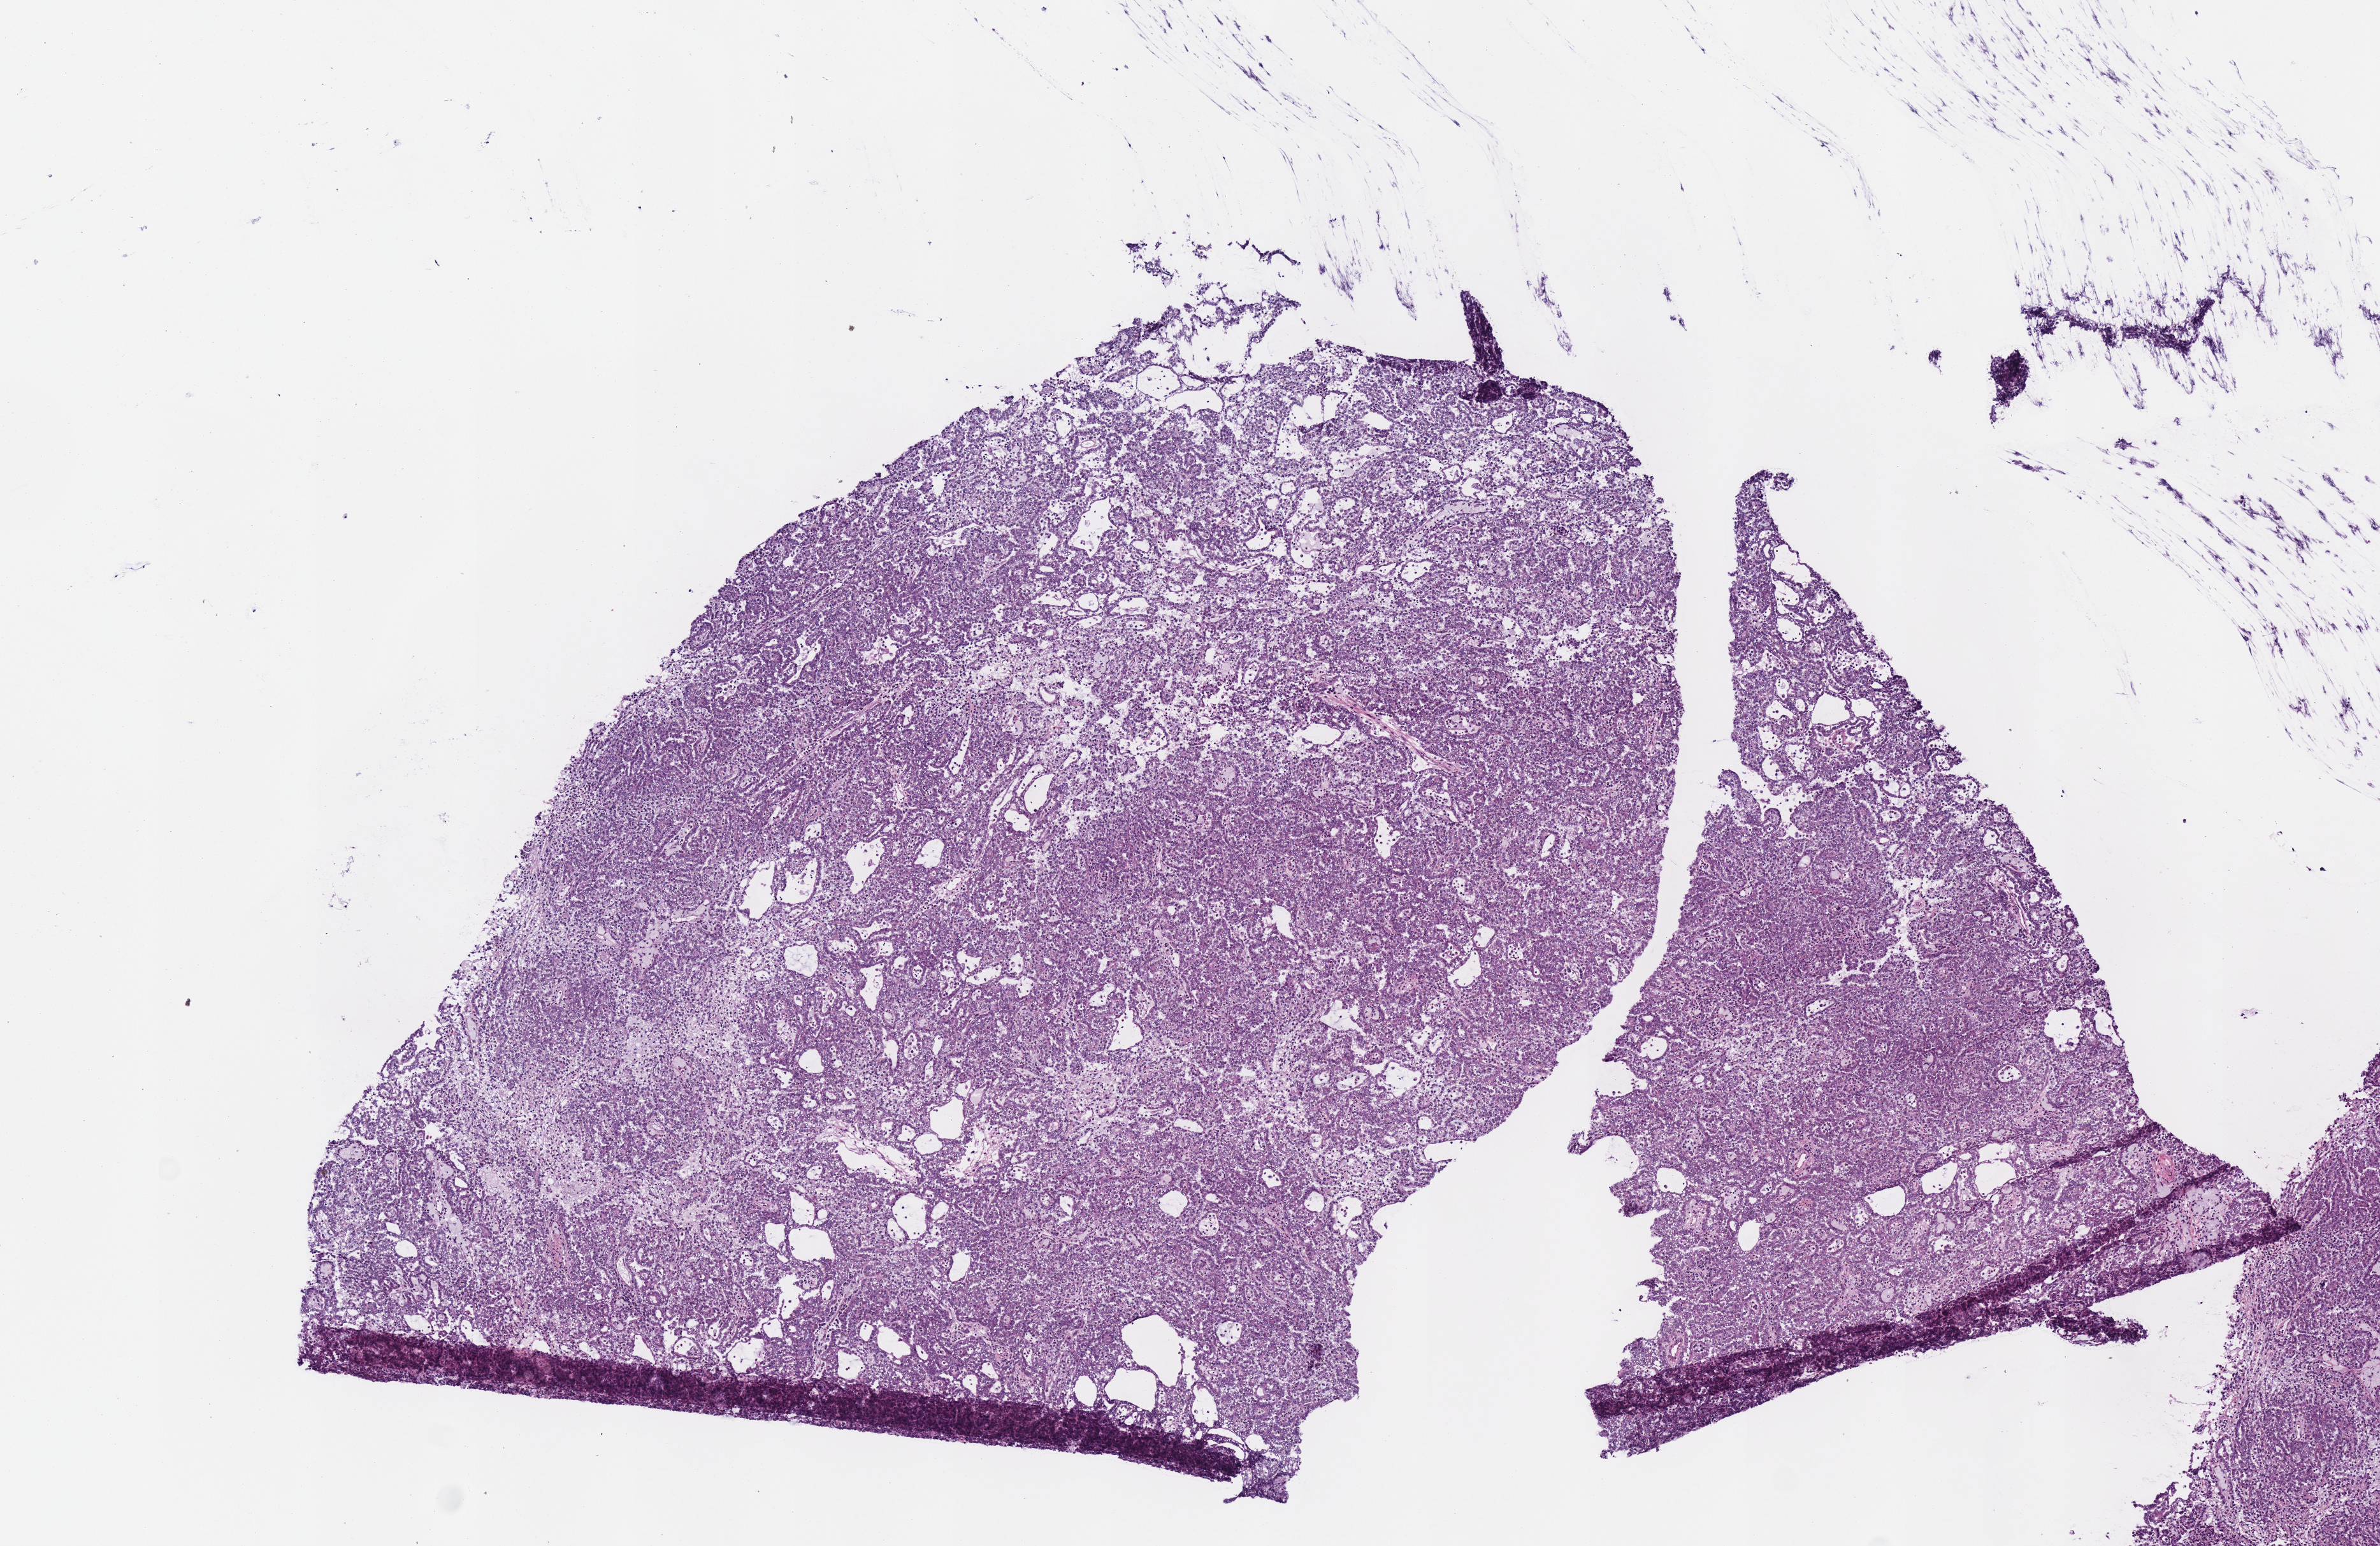
H&E-stained whole-slide image — a low-resolution overview of the entire scanned area, about 7.3 x 4.8 mm, frozen section, sample: primary tumour, kidney. Male patient; age at initial diagnosis 63 years. Slide review estimates, as recorded: tumour cells 100%, tumour nuclei 90%, normal cells 0%, stromal cells 0%, necrosis 0%. Inflammatory infiltration, as recorded: lymphocyte infiltration 3%, monocyte infiltration 3%, neutrophil infiltration 0%.
Histologic diagnosis: Papillary adenocarcinoma, NOS. AJCC pathologic stage: I (7th edition). Laterality: right. TNM: T1a NX MX.